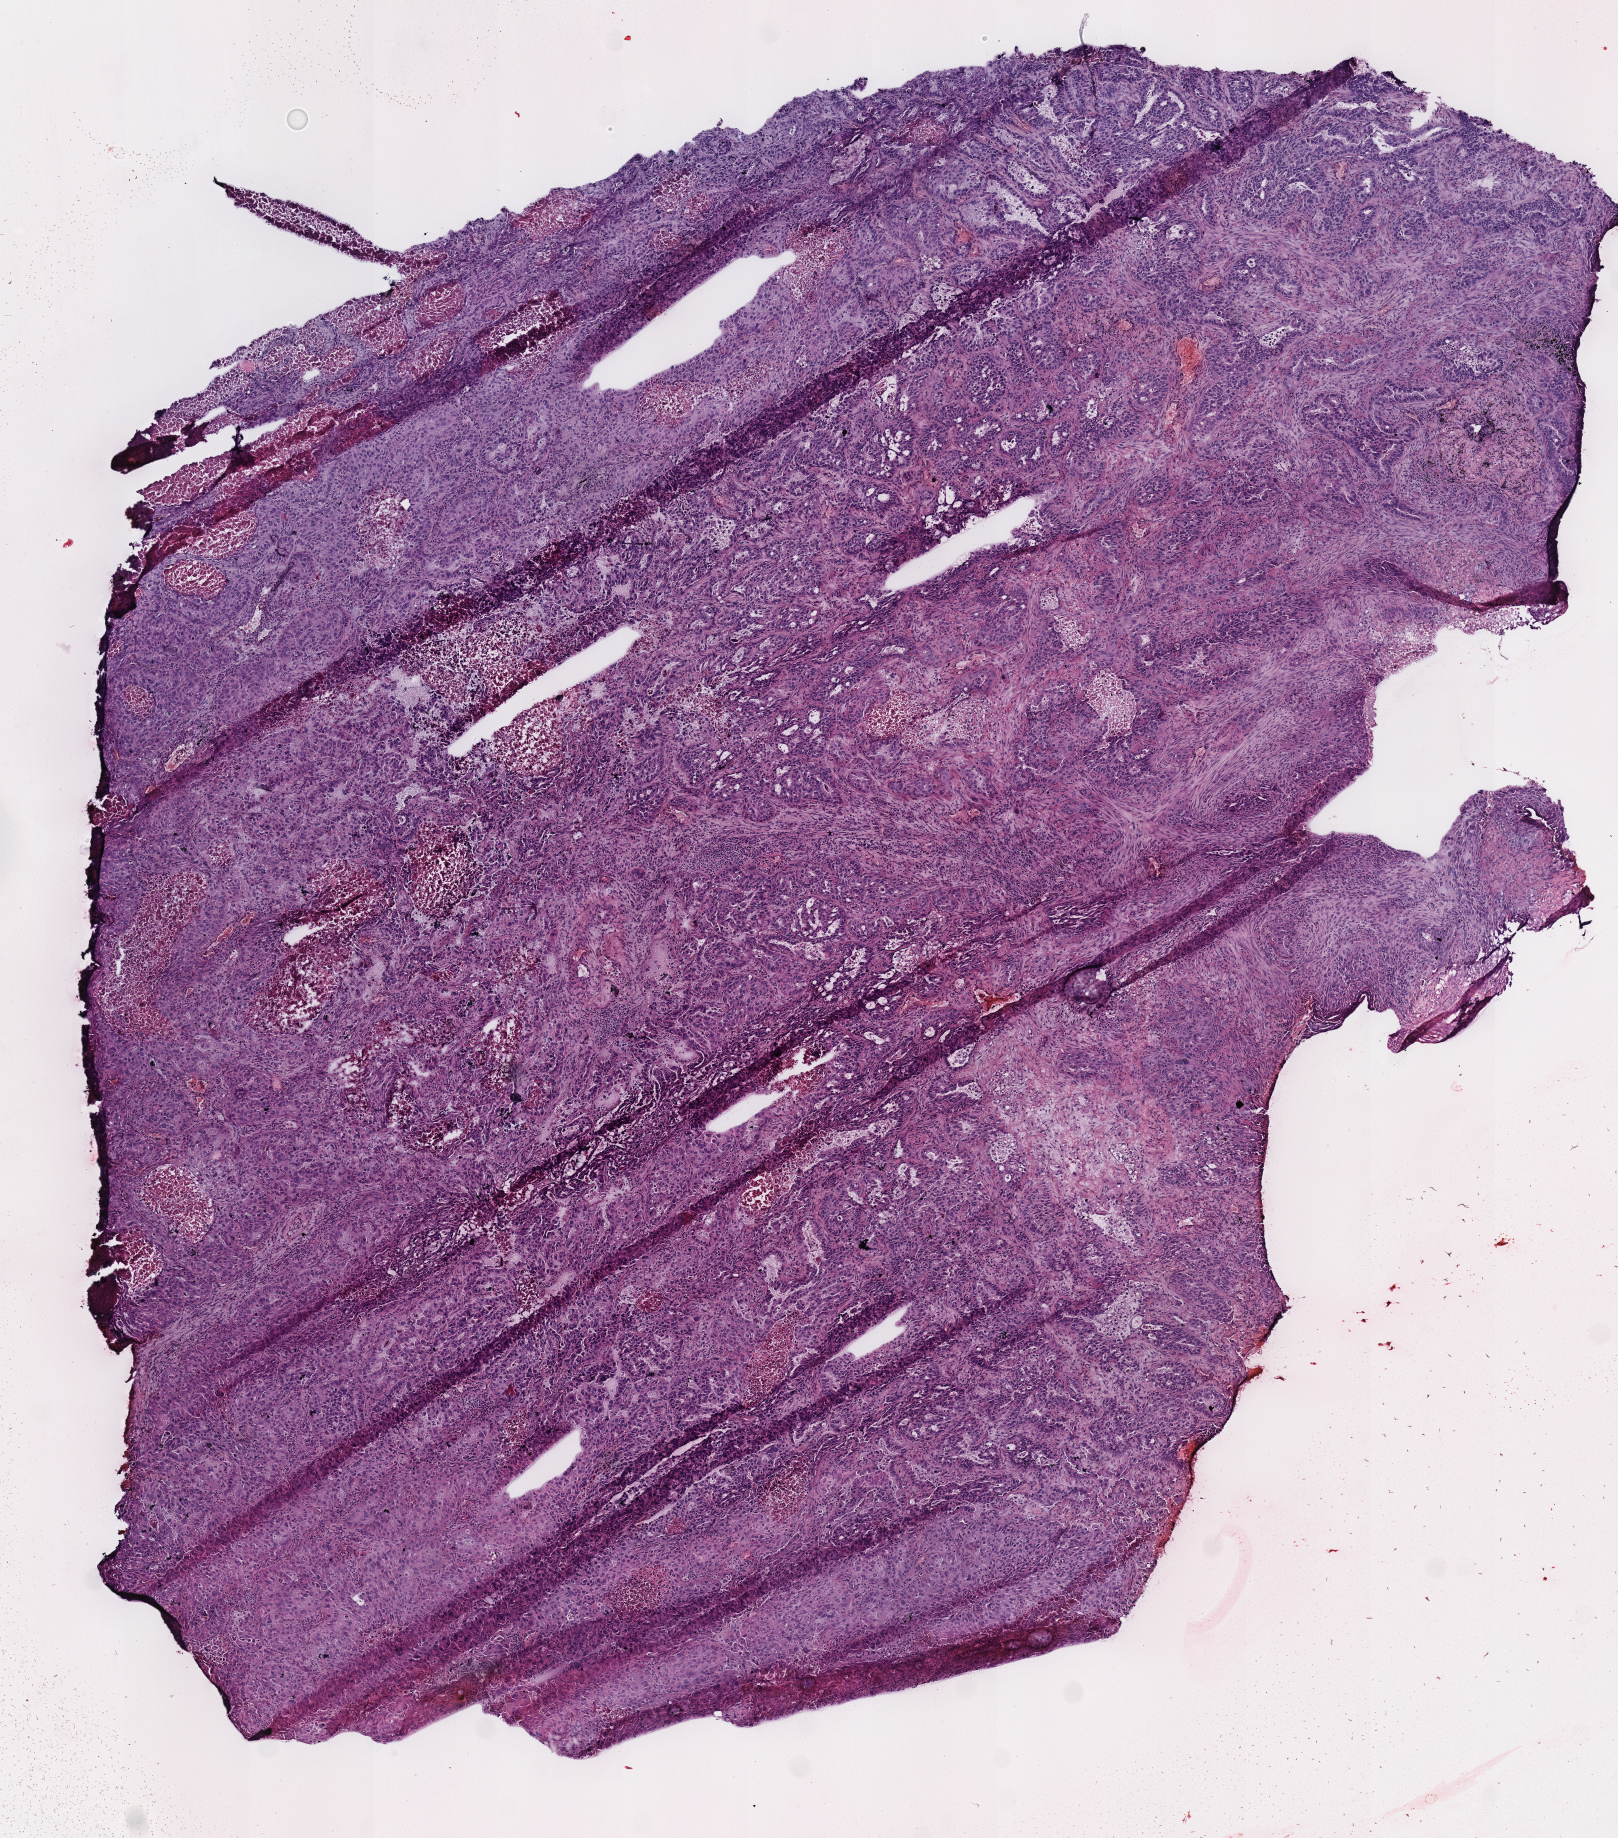
H&E whole-slide image — a low-resolution overview of the entire scanned area, about 6.4 x 7.2 mm (slide scanned at 40x), frozen section, sample: primary tumour, lung. Female patient; age at initial diagnosis 65 years. Pathologist review of this section (percent, as recorded): tumour cells 80%, tumour nuclei 70%, normal cells 0%, stromal cells 8%, necrosis 12%. Infiltration values recorded for this section: lymphocyte infiltration 12%, monocyte infiltration 3%.
- TNM: T4 N2 M0
- AJCC pathologic stage: IIIB
- diagnosis: Adenocarcinoma with mixed subtypes